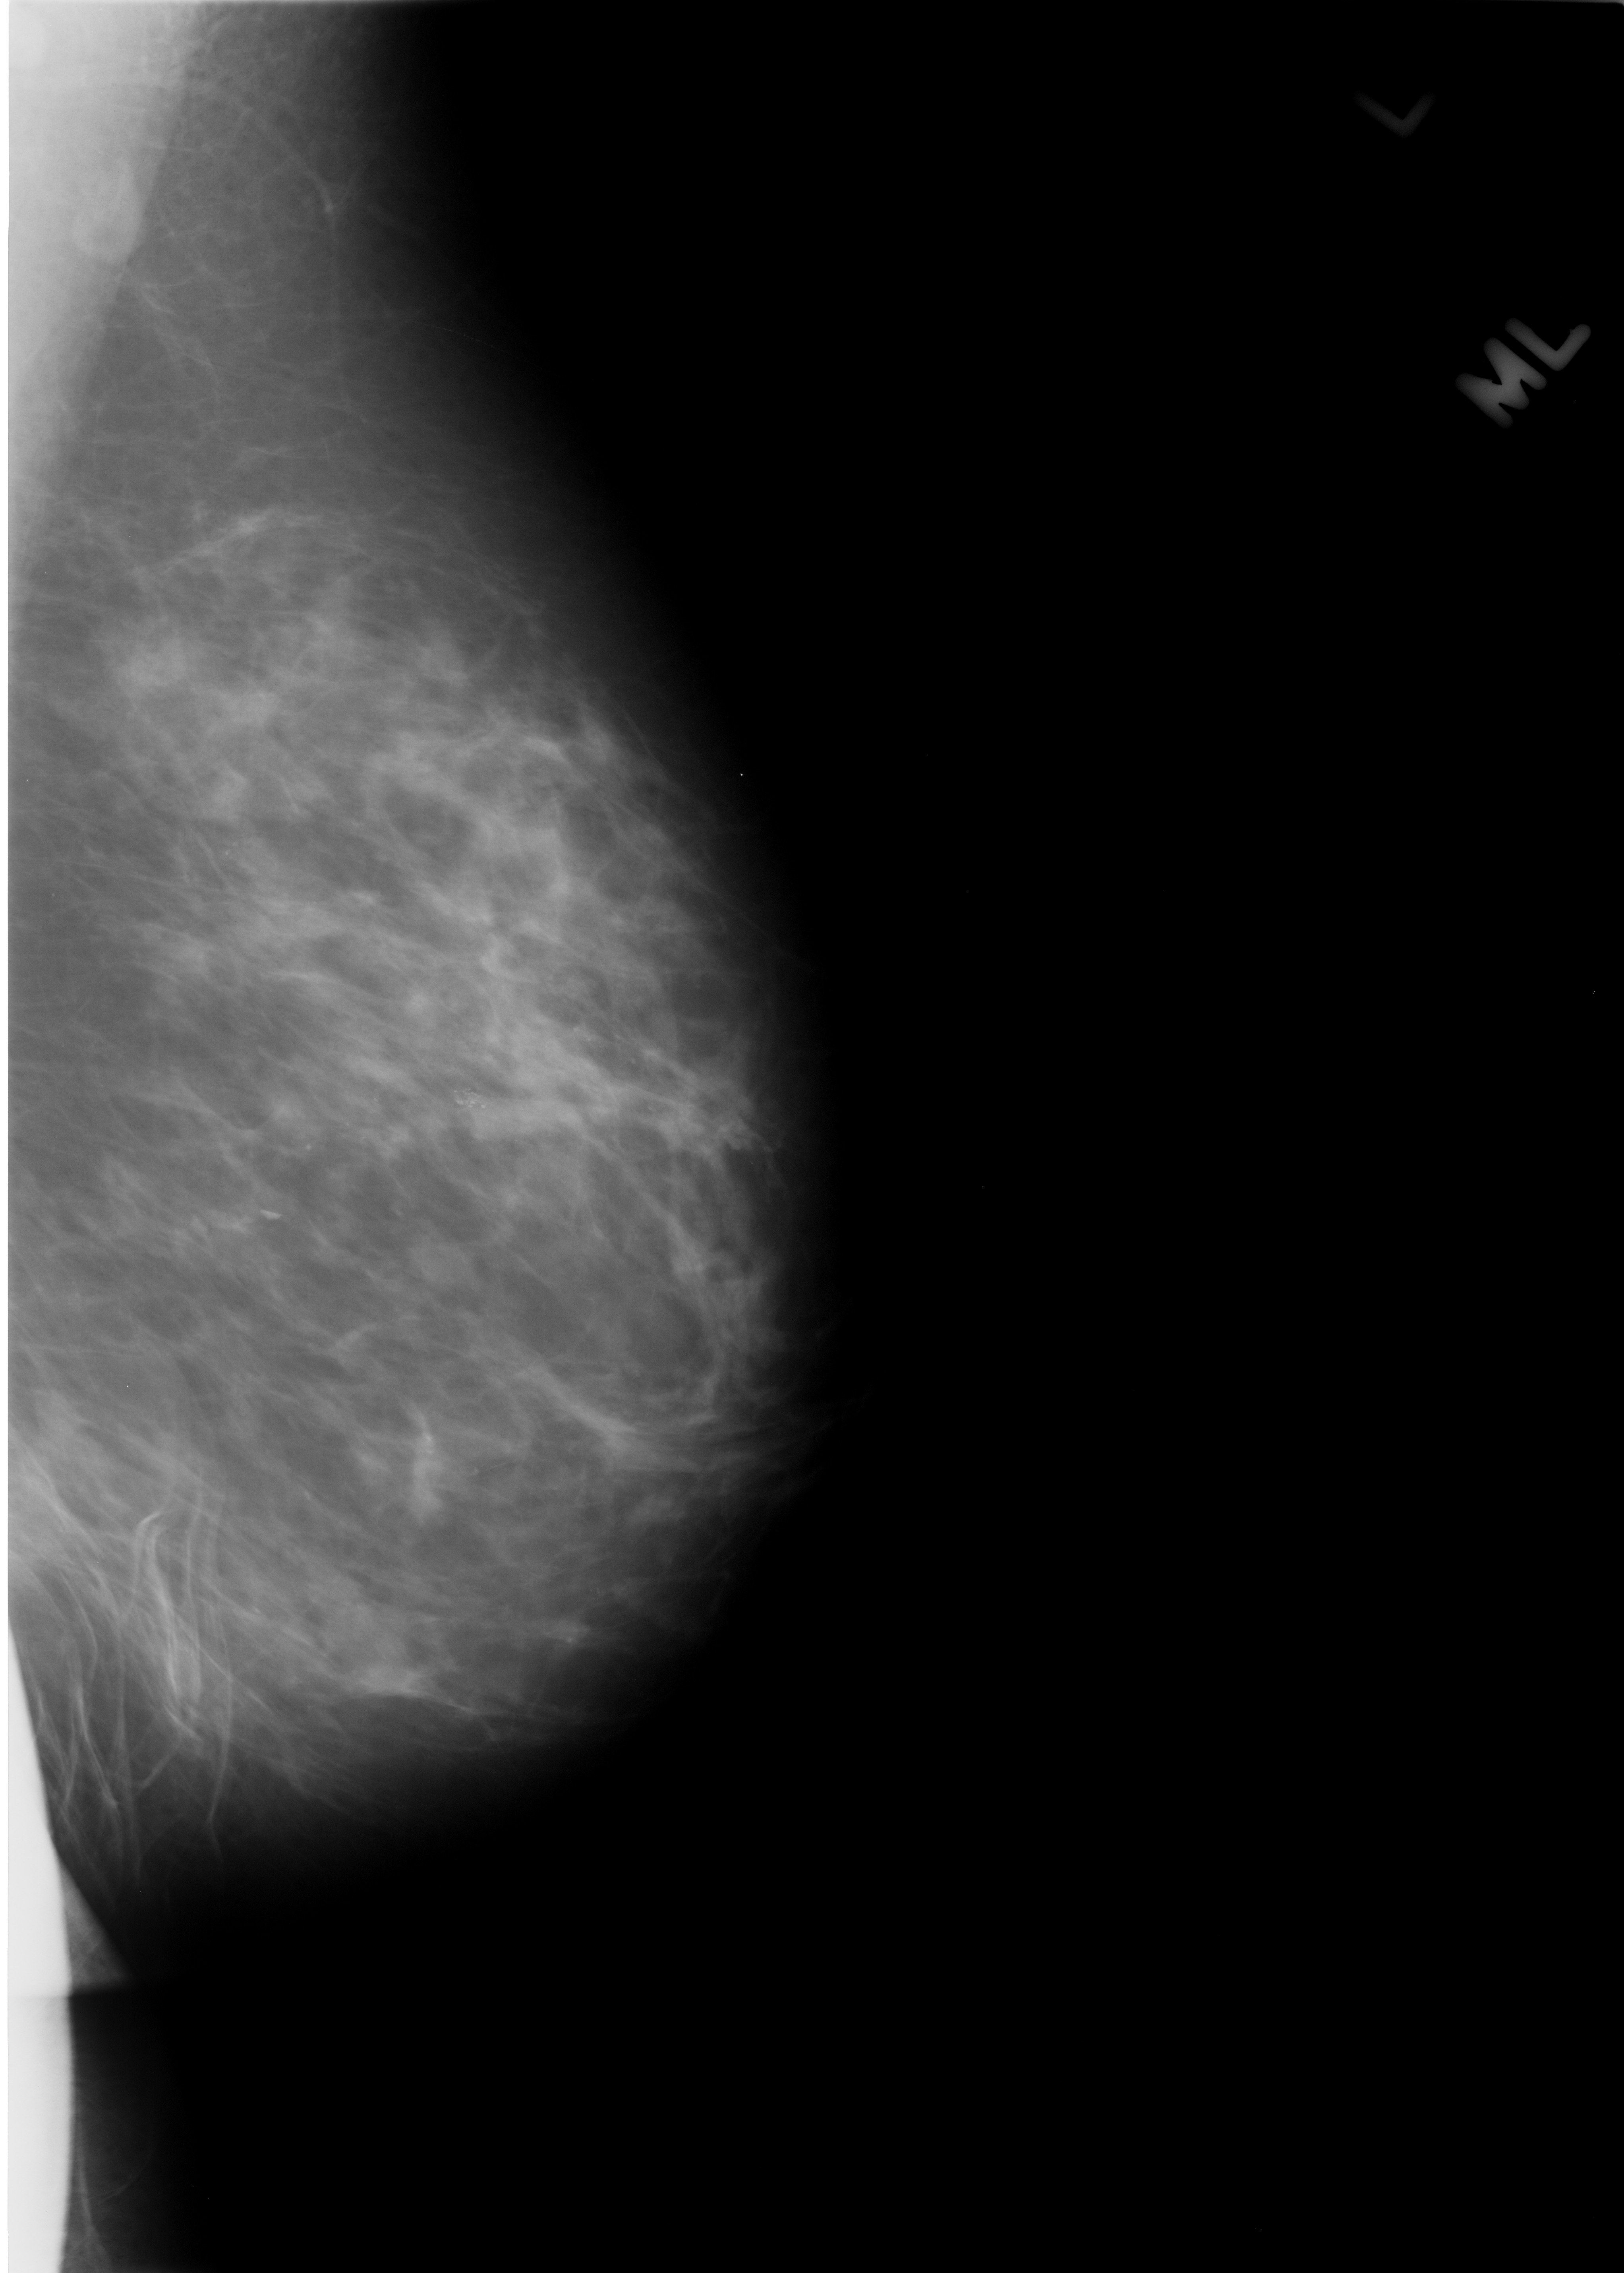
Mammogram (digitized film), left breast, mediolateral oblique (MLO) view.
Marked findings (only marked abnormalities are described; nothing is implied about the rest of the image): calcifications, morphology pleomorphic, distribution clustered; BI-RADS assessment category 4; pathology result (as recorded, not read from the image): benign.